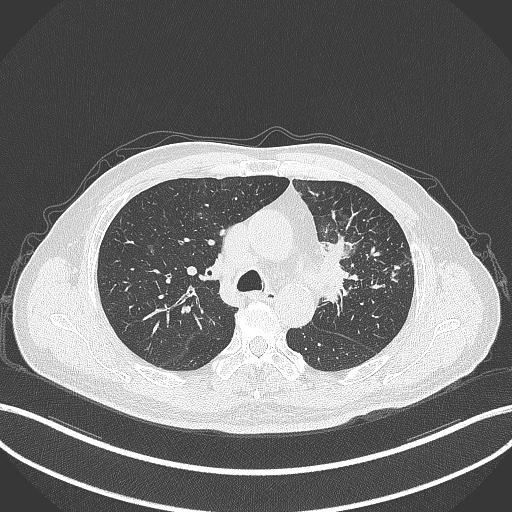
Chest CT, one axial slice; slice 233 of 386 in the series (ordered by position); reconstruction kernel B70f; 120 kVp; lung window (W 1500 / L -600 HU); 512 × 512 image matrix, field of view 400 × 400 mm. Male patient, age 69 years. Case-level facts recorded for this patient, not image findings: clinical TNM (as recorded): T2a N2 M0; histopathological grade: G2-3.
Annotated regions visible in this slice (rectangle marked by the reading radiologist):
- lung tumour (recorded histology: adenocarcinoma): bounding box (x1, y1, x2, y2) in pixels: (315, 235, 363, 303)